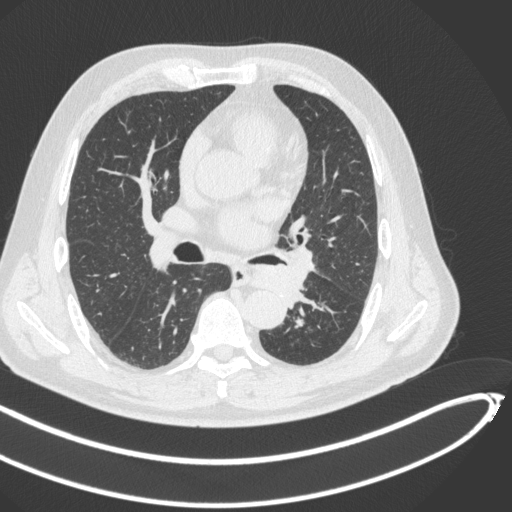
Chest CT, one axial slice; slice 254 of 466 in the series (ordered by position); lung window (W 1500 / L -600 HU); 1 mm slice thickness; 512 × 512 image matrix, field of view 400 × 400 mm. Patient: male, 64 years. Case-level facts recorded for this patient, not image findings: clinical TNM (as recorded): T1c N0 M0; histopathological grade: G2.
Structures marked on this image (bounding box drawn by a radiologist):
- lung tumour (recorded histology: squamous cell carcinoma): bounding box (x1, y1, x2, y2) in pixels: (252, 264, 308, 304)